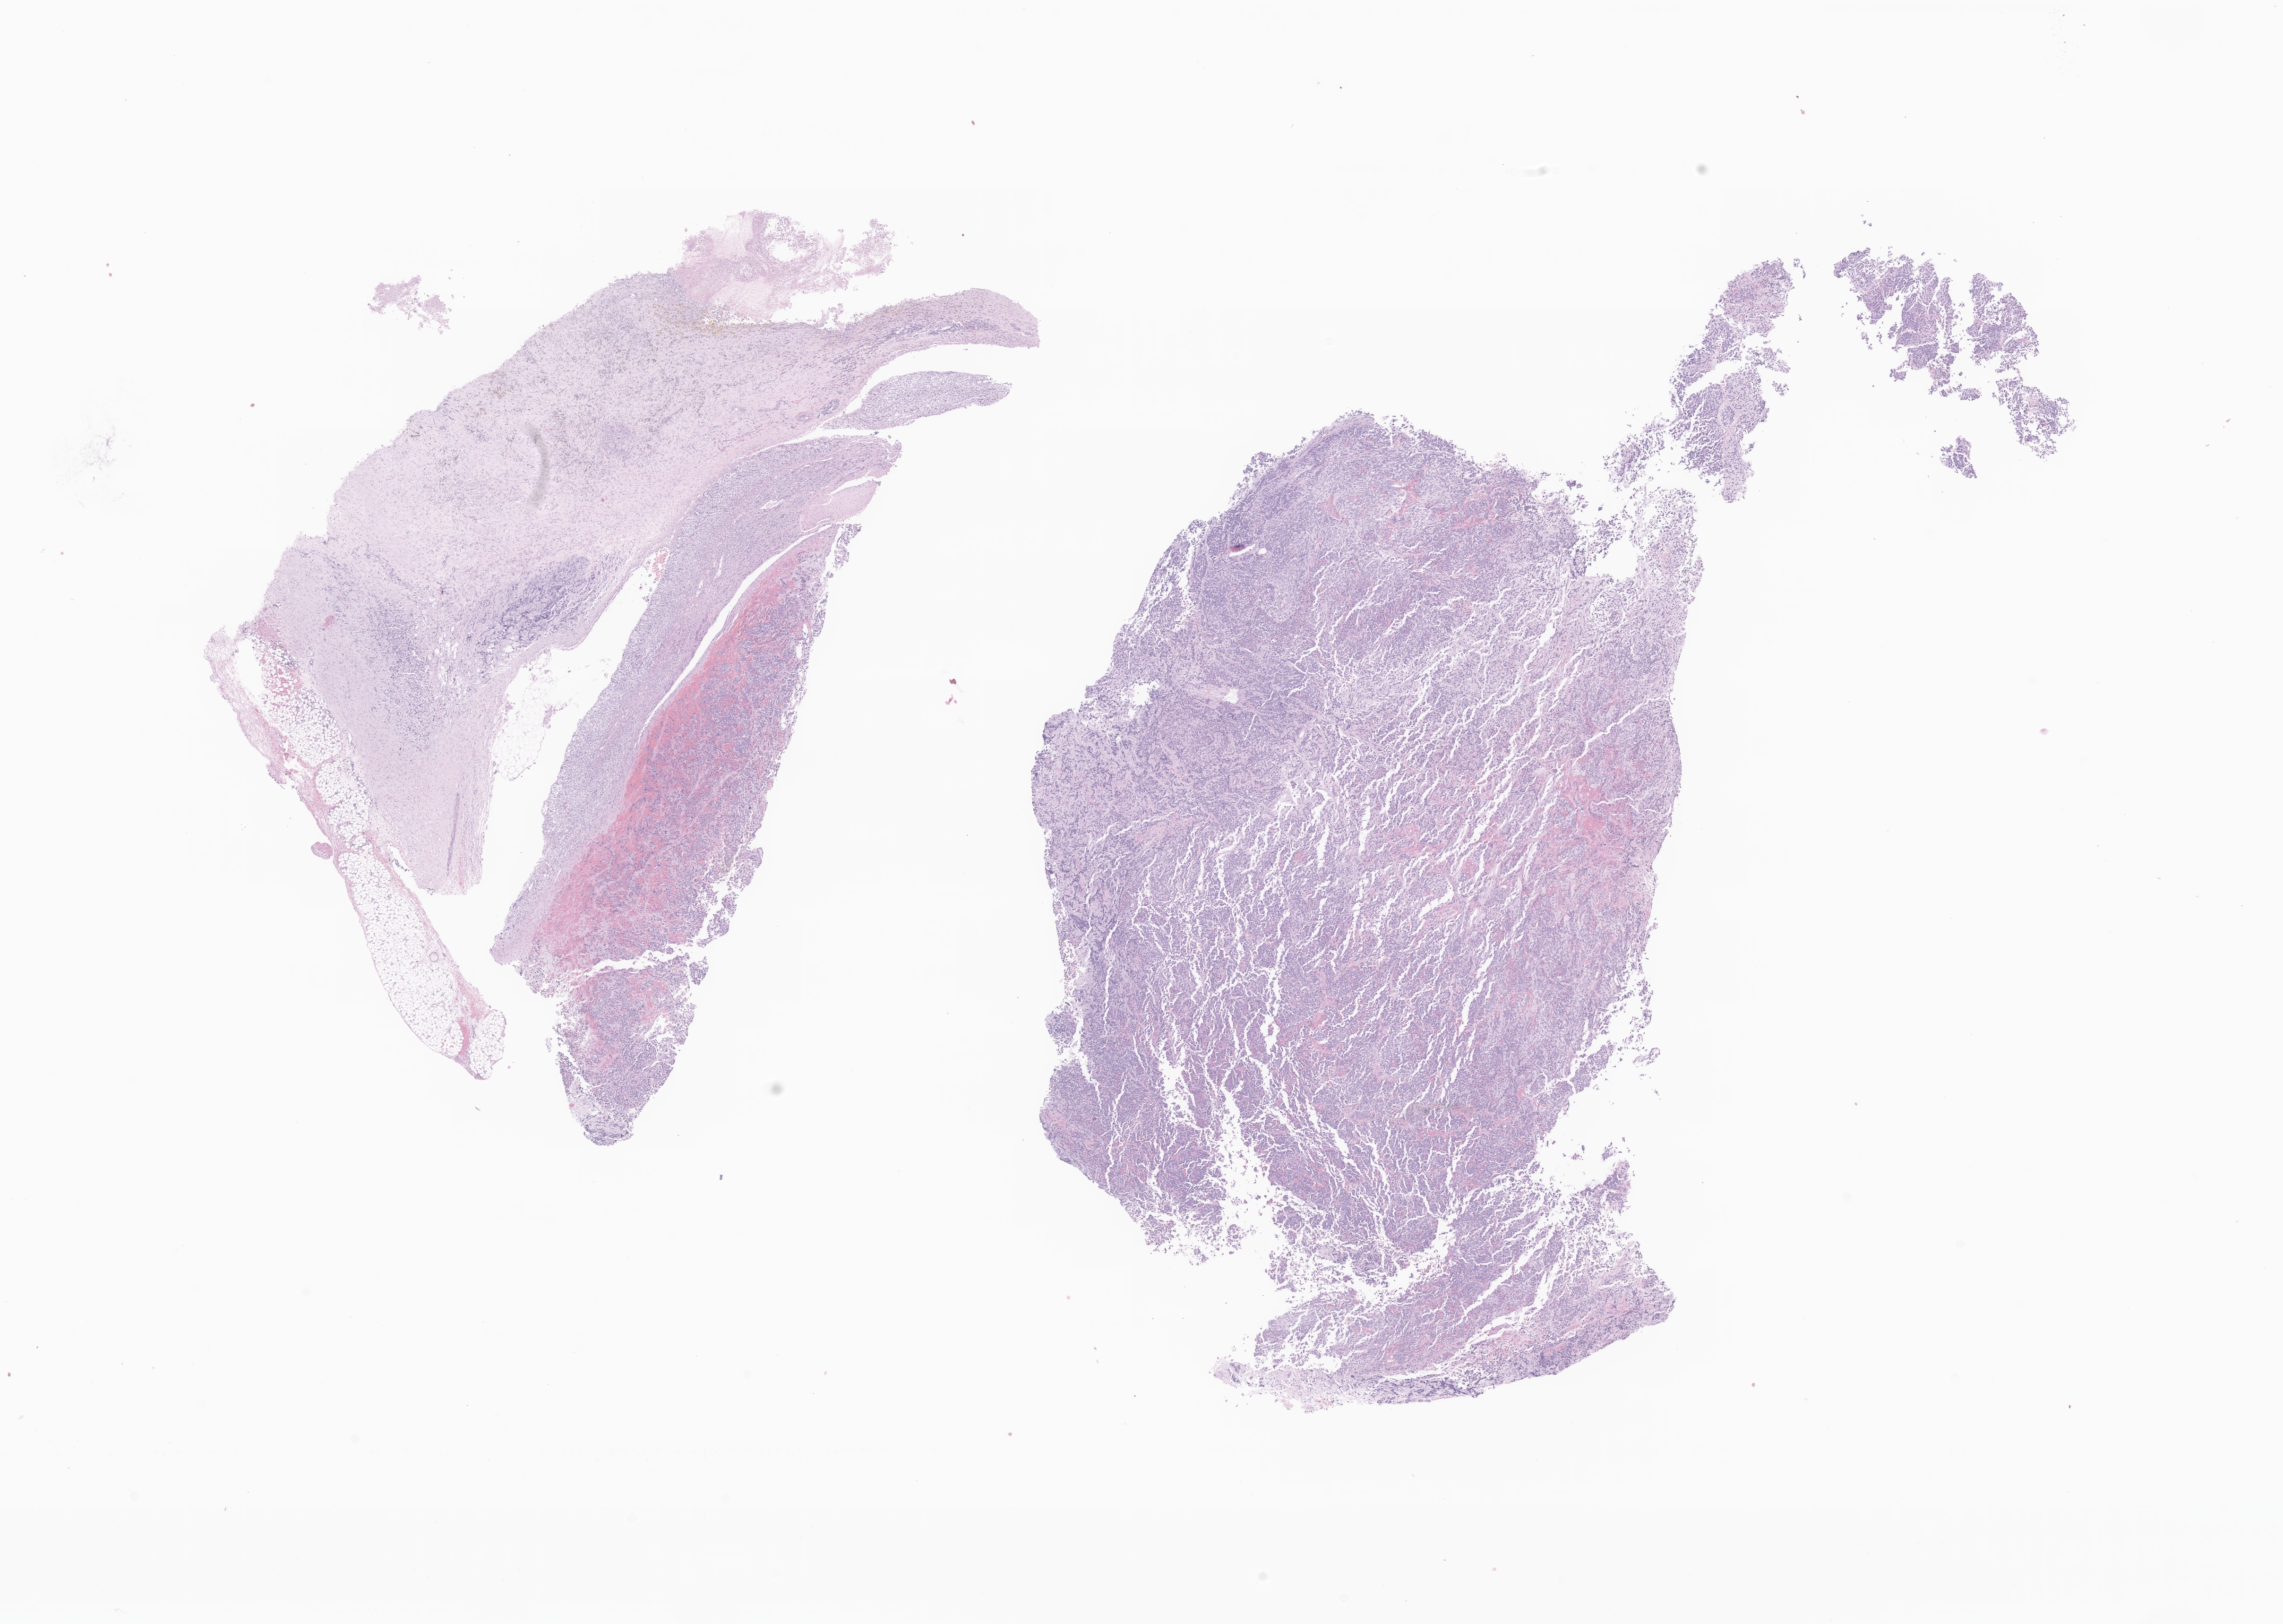
Whole-slide image, hematoxylin and eosin (H&E) stain of tumor tissue from the adrenal gland — low-resolution overview of the scanned area, about 20.4 x 14.5 mm; formalin-fixed, paraffin-embedded (FFPE) tissue. Patient male; age 326 days.
Diagnosis (ICD-O-3 morphology term): Neuroblastoma, NOS.